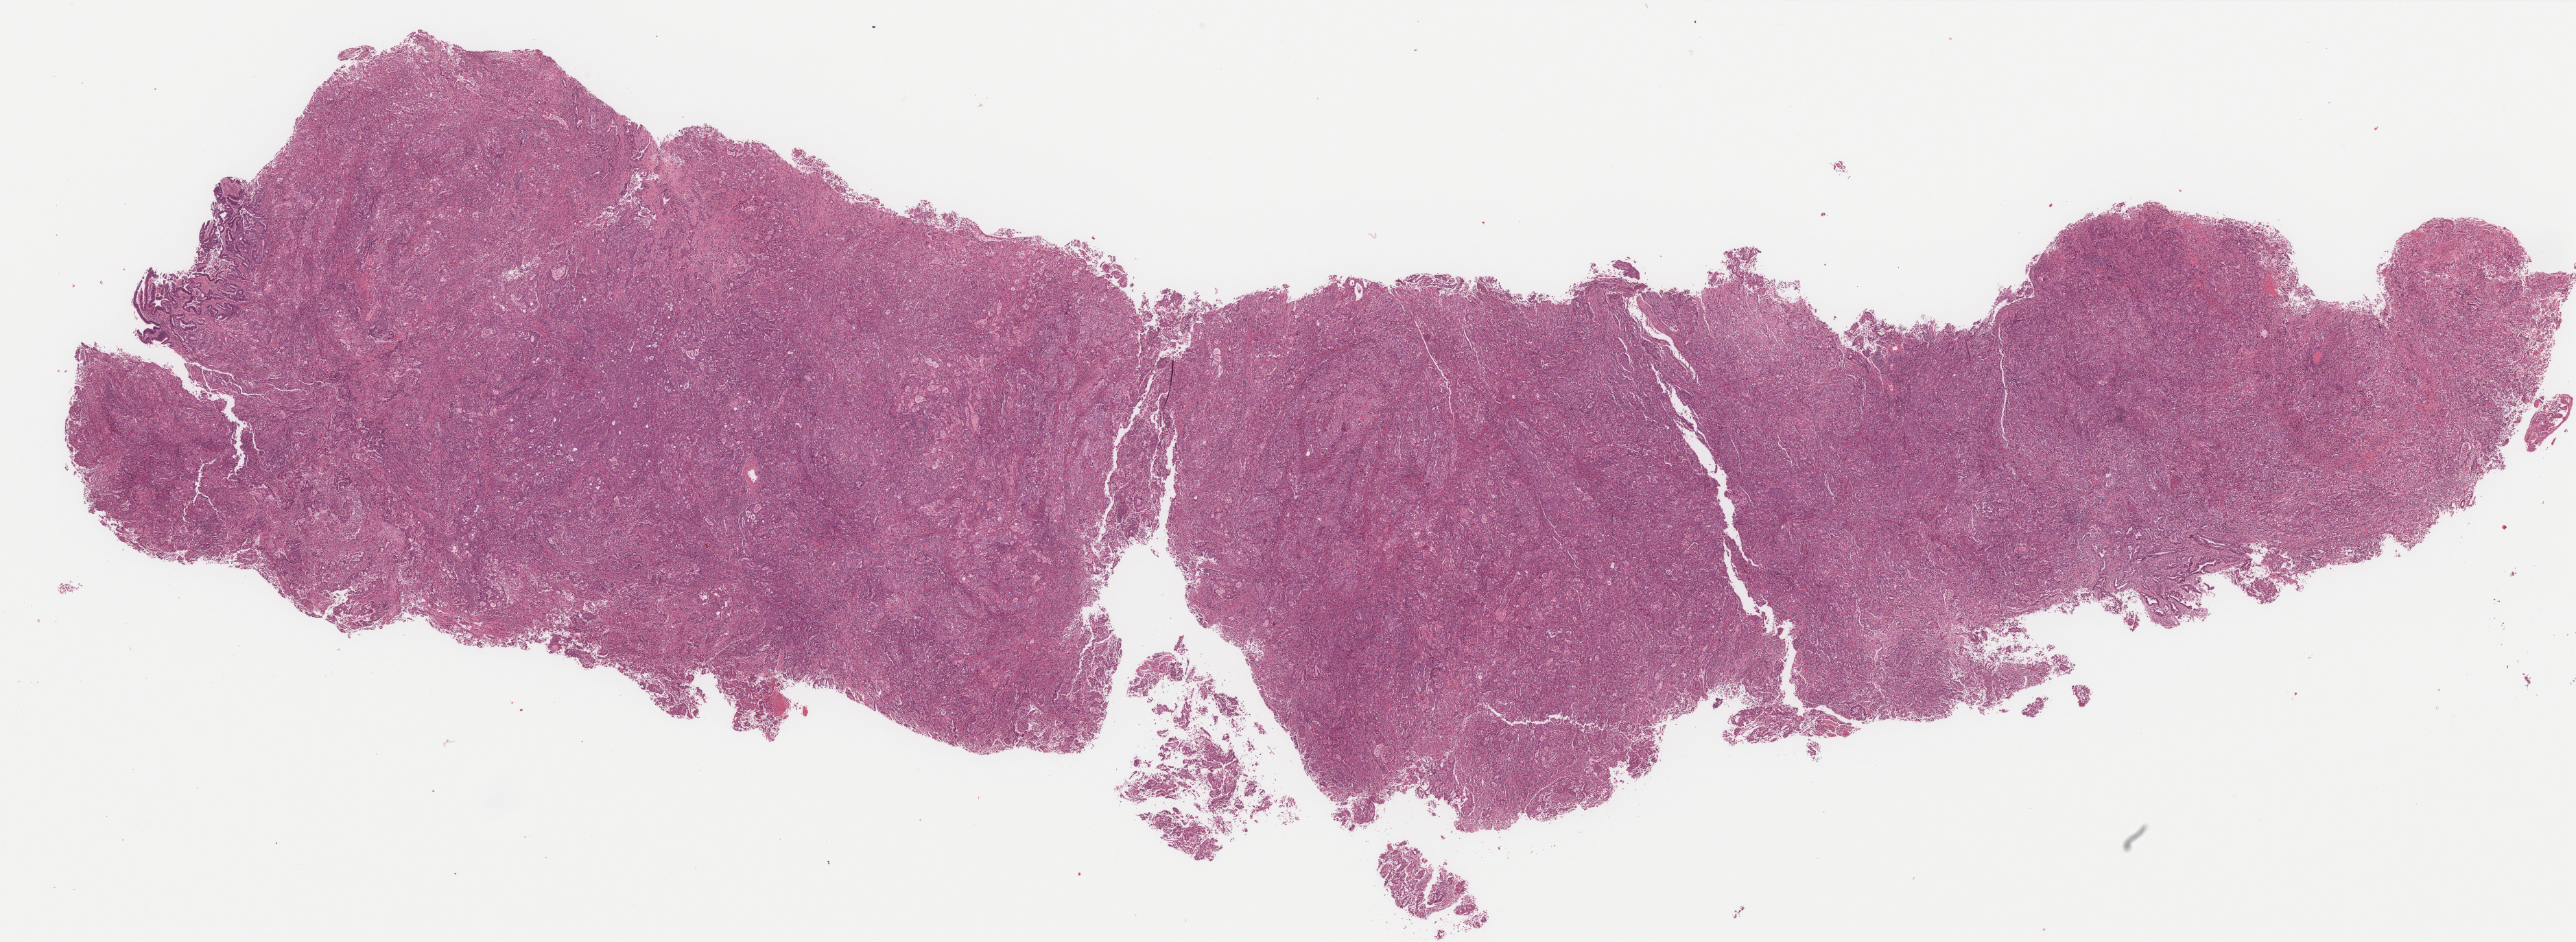
Hematoxylin and eosin (H&E) stained whole-slide image — low-resolution overview of the scanned area, about 30.2 x 11.1 mm. Formalin-fixed paraffin-embedded (FFPE) diagnostic section. Sample: primary tumour, uterus. Female, age 51 years at initial diagnosis. Histologic grade: G3 (poorly differentiated).
FIGO stage: IIIC1. Pathologic diagnosis: Endometrioid adenocarcinoma, NOS (endometrium).